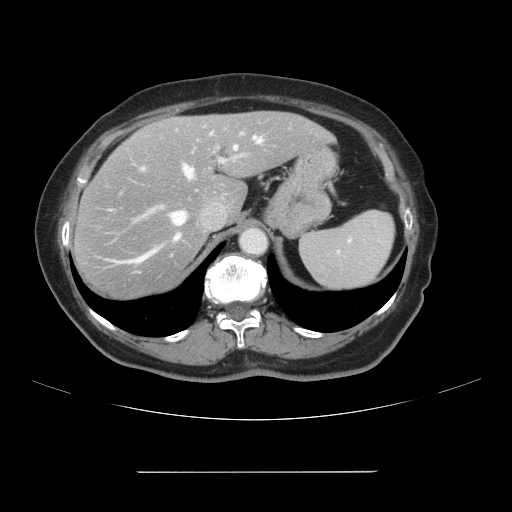
Contrast-enhanced abdominal CT, one axial slice. Position 76 of 111 along the scan axis. Intravenous contrast given. Soft-tissue window (W 400 / L 40 HU). 512 × 512 image matrix, field of view 400 × 400 mm. Female patient, age 74 years. Case-level facts recorded for this patient, not image findings: diagnosis: colorectal cancer liver metastases, imaged before liver resection; multiple liver metastases: yes; largest metastasis: 1.1 cm.
Annotated regions visible in this slice (outlined manually by an expert reader):
- hepatic veins: bounding box (x1, y1, x2, y2) in pixels: (105, 136, 262, 273)
- liver: (74, 112, 333, 301)
- planned liver remnant (the part of the liver to remain after resection): (157, 112, 332, 219)
- portal vein (with intrahepatic branches): (142, 134, 243, 208)